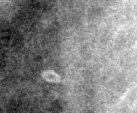
Cropped region of a digitized screen-film mammogram centred on a radiologist-marked abnormality; right breast; MLO view.
Calcifications, morphology lucent center; BI-RADS assessment category 2; subtlety rating 3 on a 1 (subtle) to 5 (obvious) scale; benign; no additional work-up was recommended (benign without callback).